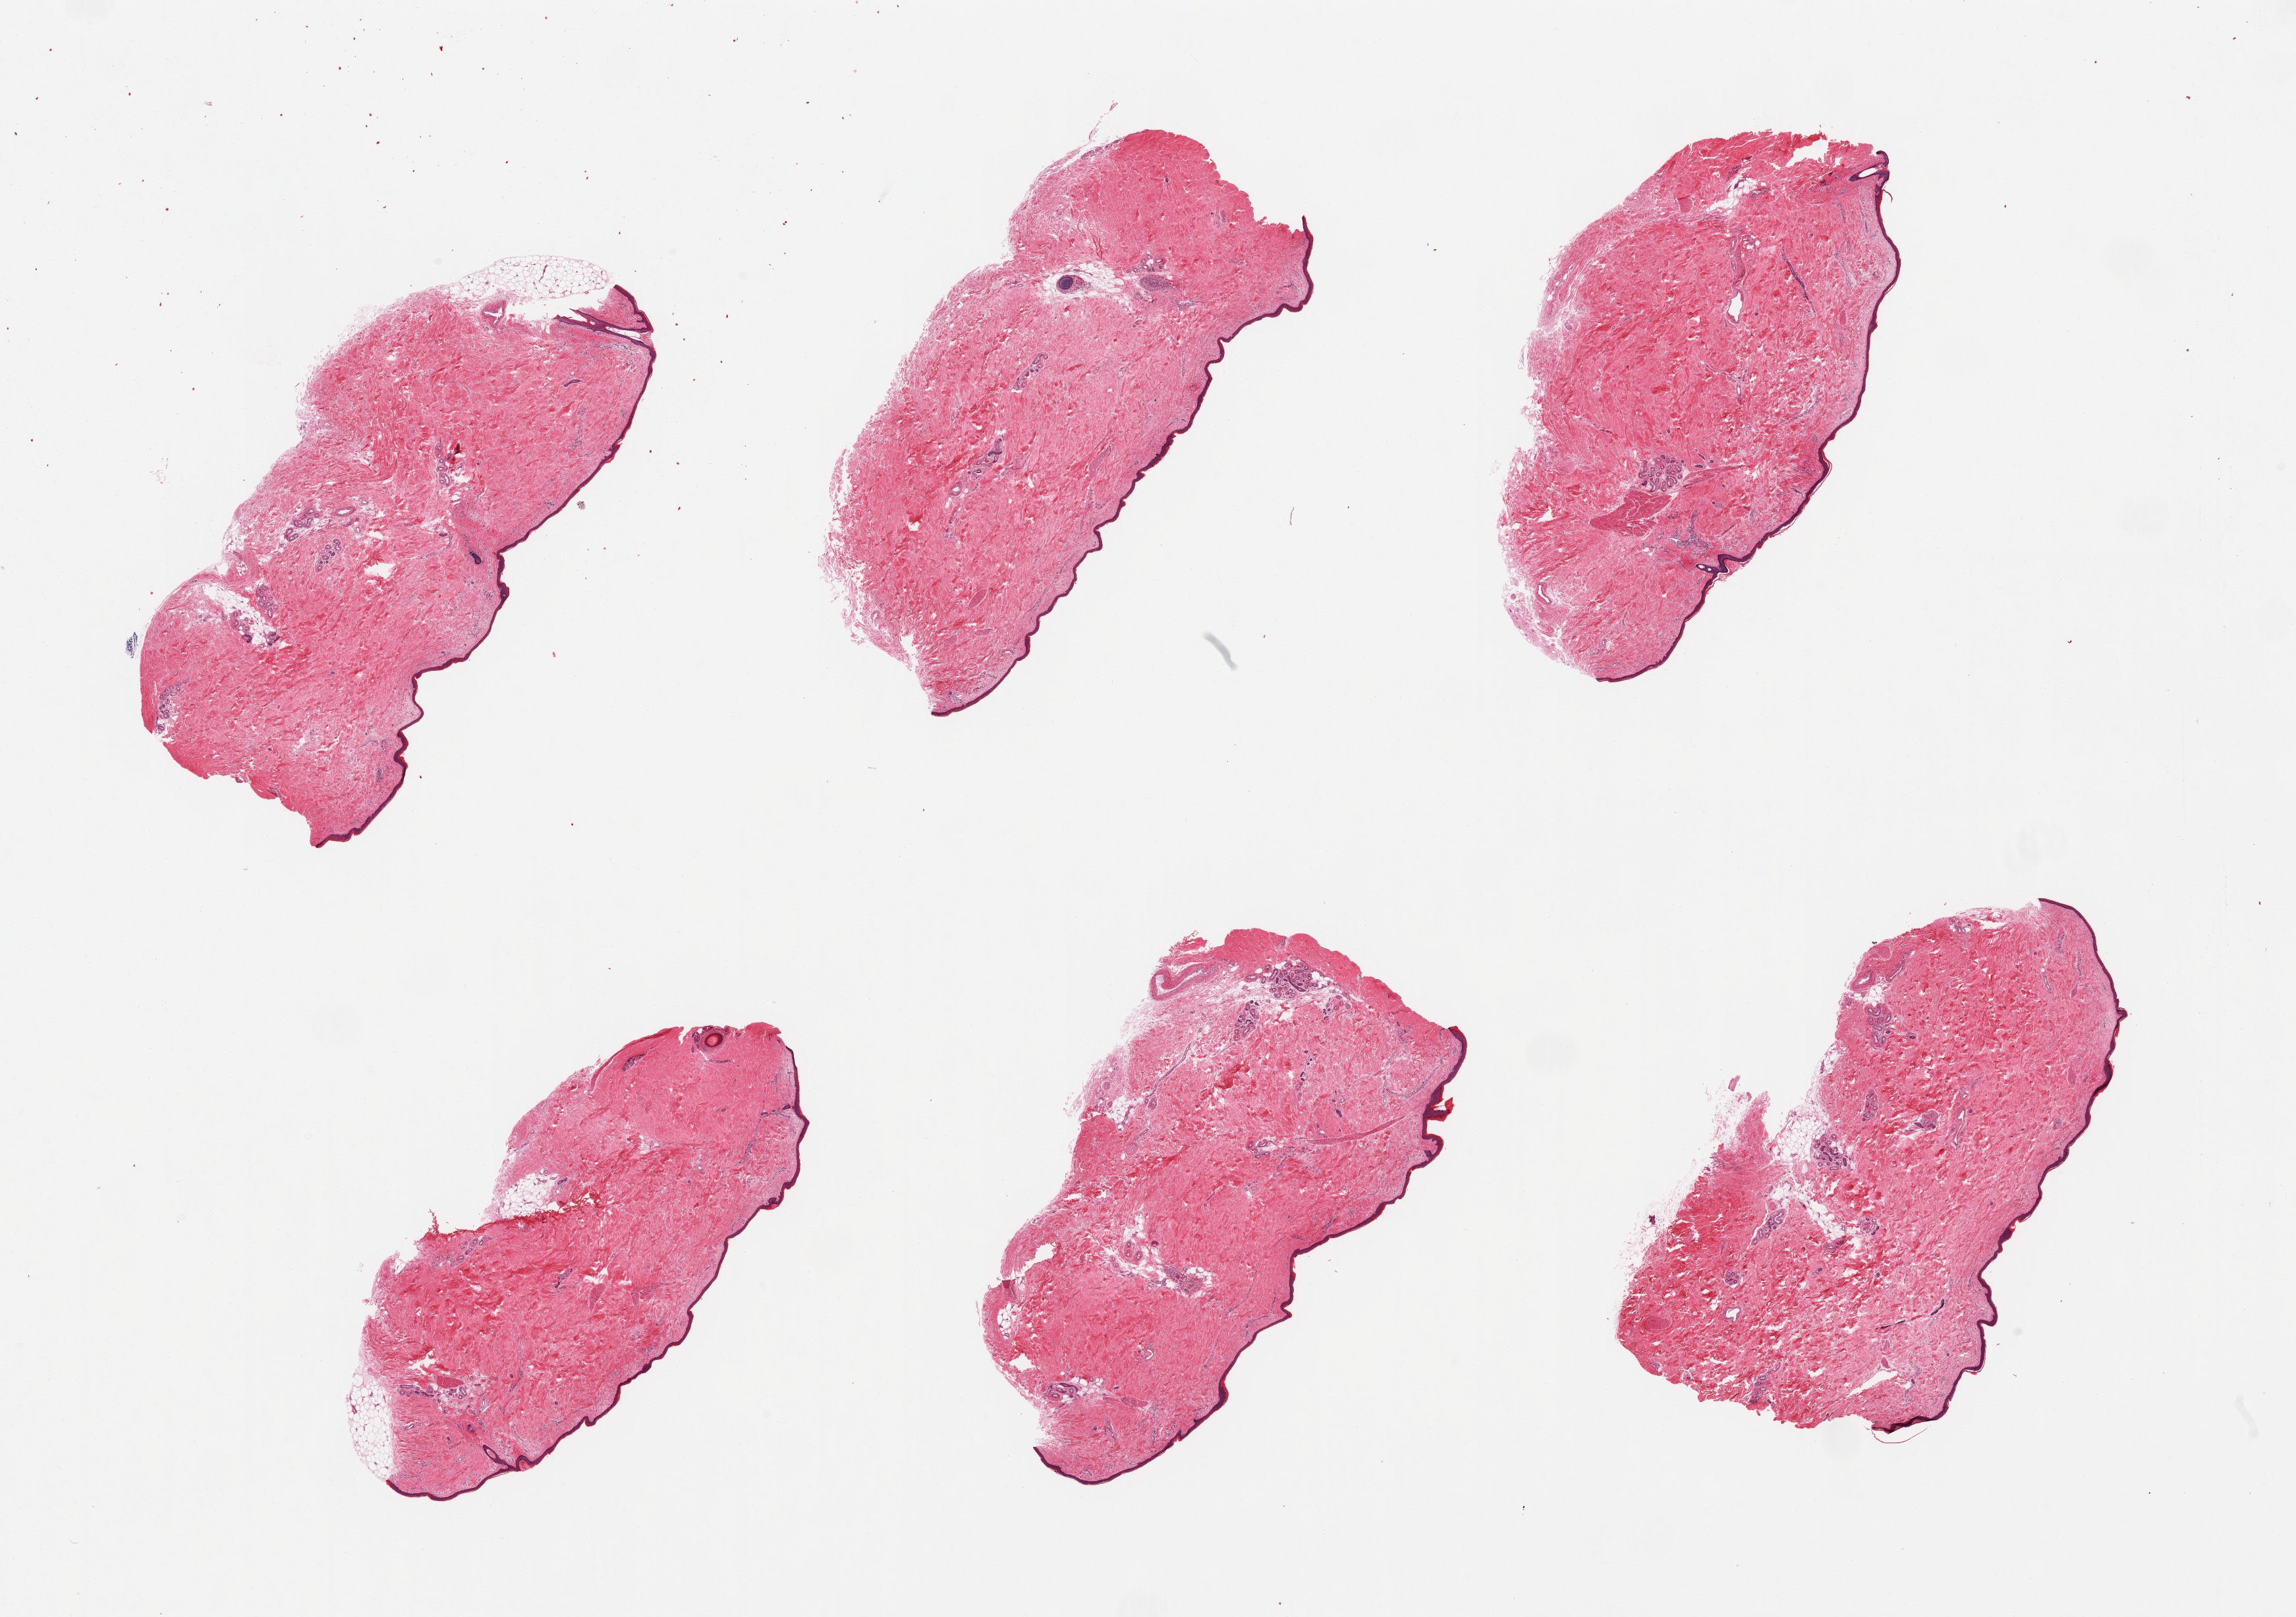
Whole-slide image, H&E stain — low-resolution overview of the scanned area, about 27.6 x 19.4 mm. PAXgene-fixed, paraffin-embedded tissue. Section of skin of lower leg (target tissue). Donor tissue sample. Male donor.
• reviewer comment on this tissue sample: 6 pieces, no dermal fat; squamous epithelium is ~30-40 microns